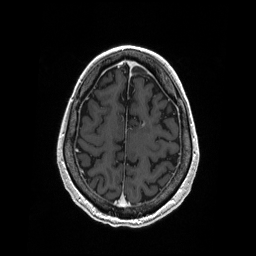
Brain MRI from a brain-tumour surgery series, one axial slice; slice 59 of 208 in the series (ordered by position); T1-weighted post-contrast; 1 mm slice thickness; 256 × 256 image matrix, field of view 256 × 256 mm. From the clinical record (not read from this slice): histopathology: Primary diffuse large B-cell lymphoma; tumour location: Left Corpus Callosum (Frontal).
Structures marked on this image (manually delineated by an expert):
- tumour: box from (x=142, y=120) to (x=146, y=127) px